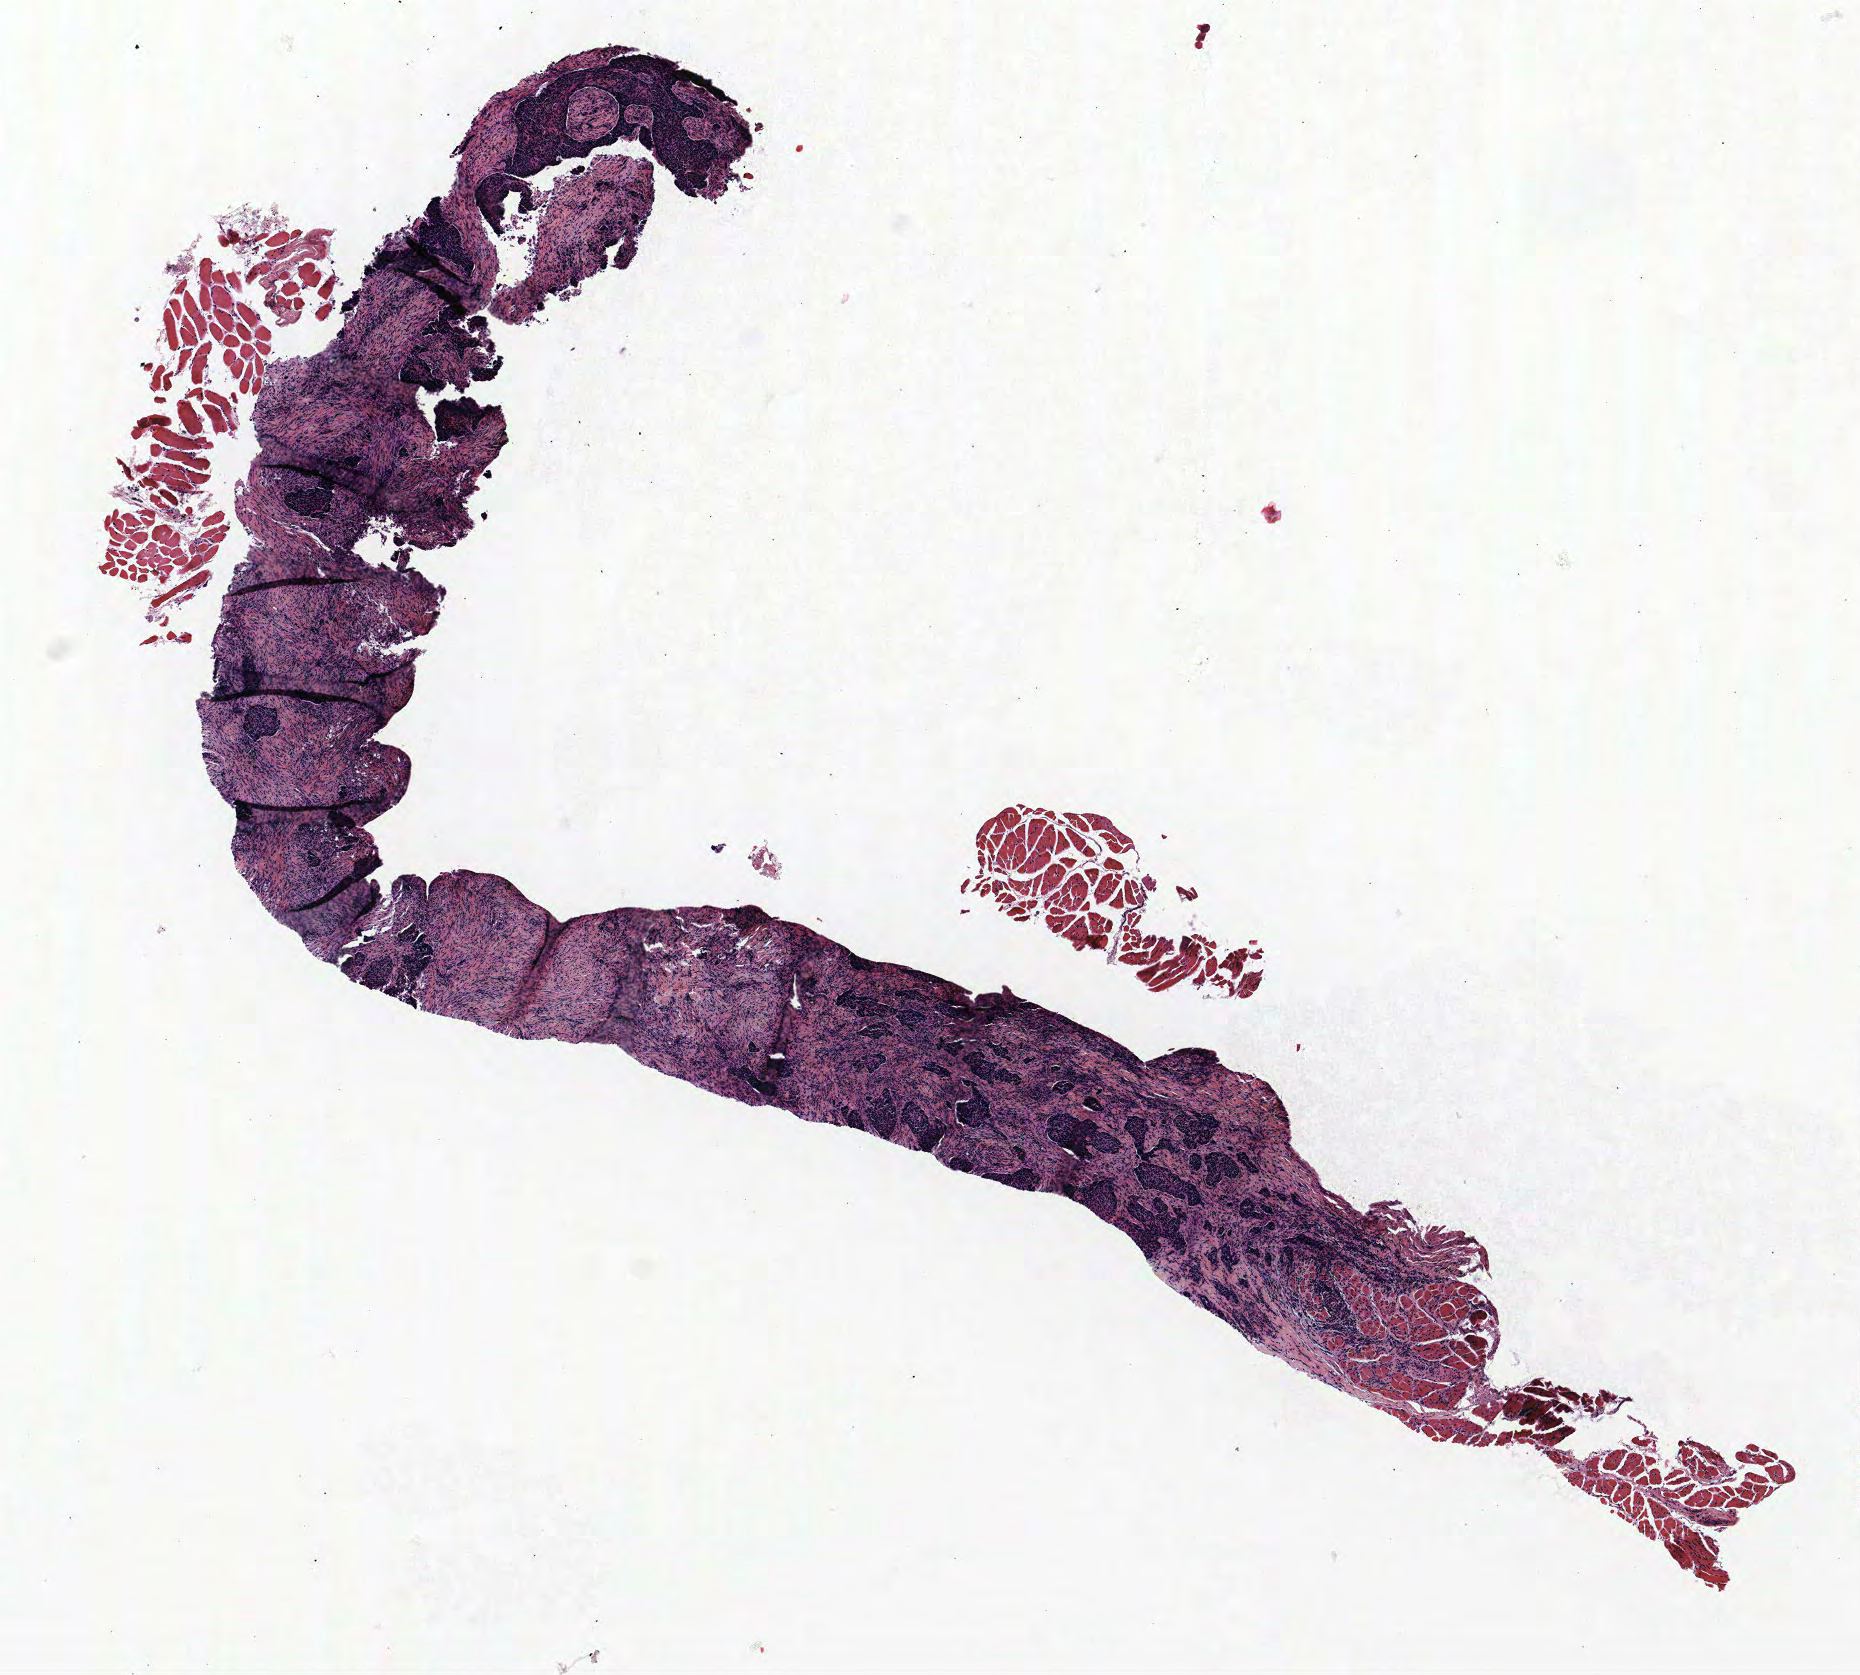
H&E-stained whole-slide image, low-resolution overview of the scanned area, about 7.4 x 6.7 mm. FFPE section. Lung. Female, age 68 at enrolment. Current smoker at enrolment. Grade: cannot be assessed (GX).
Tumour size (pathology): 30 mm. Participant's lung-cancer diagnosis: Squamous cell carcinoma, NOS. Primary tumour location (clinical record): right lower lobe. Stage (AJCC 6th edition): IV.